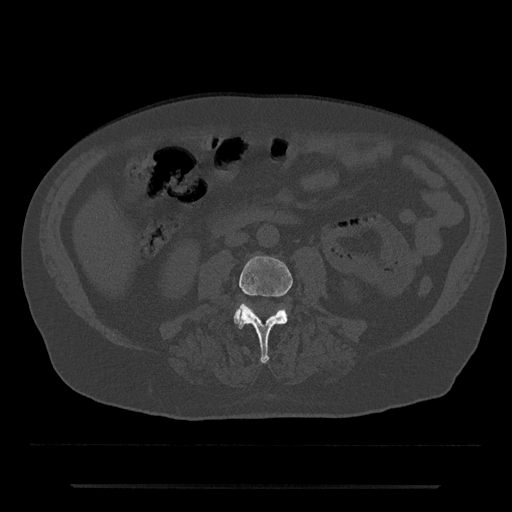
CT including the spine, one axial slice; position 398 of 797 along the scan axis; reconstruction kernel Br40s/3; 120 kVp; bone window (W 1800 / L 400 HU); 0.5 mm slice thickness; 512 × 512 image matrix. Patient: male, 80 years. From the clinical record (not read from this slice): primary cancer: prostate.
Structures marked on this image (semi-automatically segmented with operator editing):
- L3 vertebra: box from (x=239, y=256) to (x=293, y=363) px
- L4 vertebra: (x=233, y=306)–(x=288, y=326)